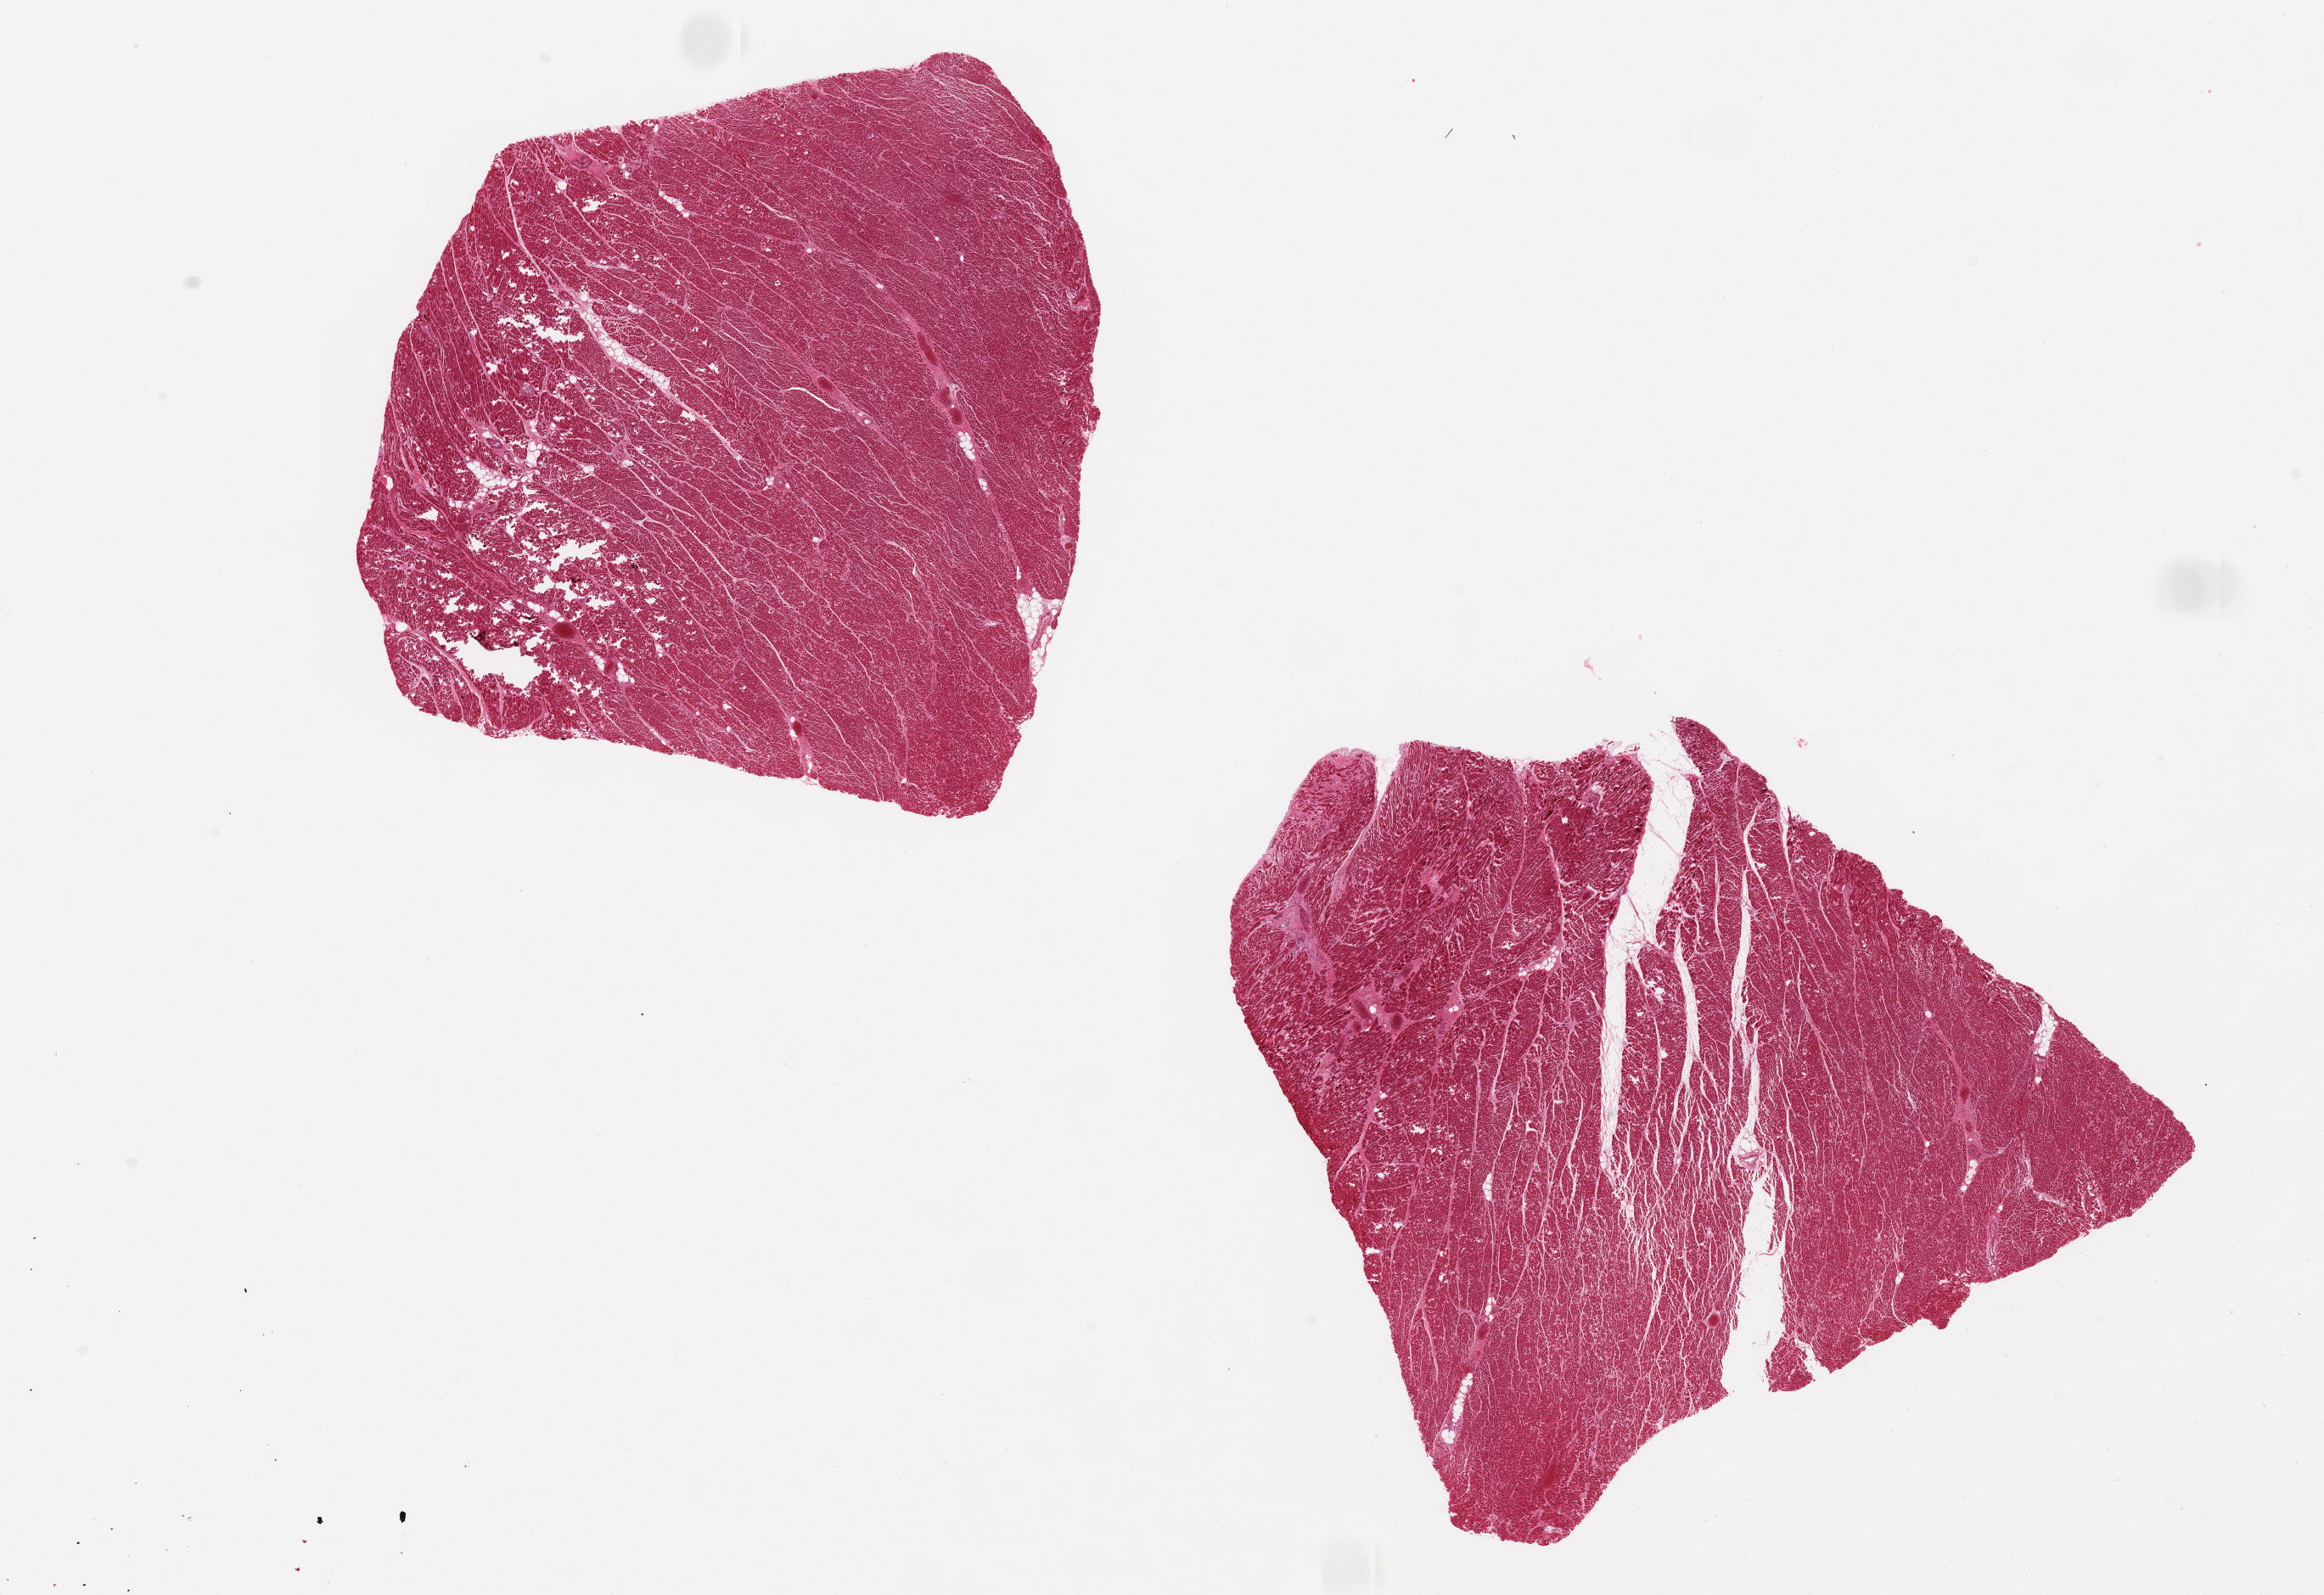
Digitized hematoxylin and eosin (H&E)-stained section, brightfield — whole scanned area (about 21.7 x 14.9 mm, slide scanned at 20x) shown as a low-resolution overview. PAXgene-fixed, paraffin-embedded tissue. Section of heart (target tissue). Donor tissue sample.
Review note (as recorded): 2 ~7.5x6.5 mm aliquots, areas of poor/under-fixation.